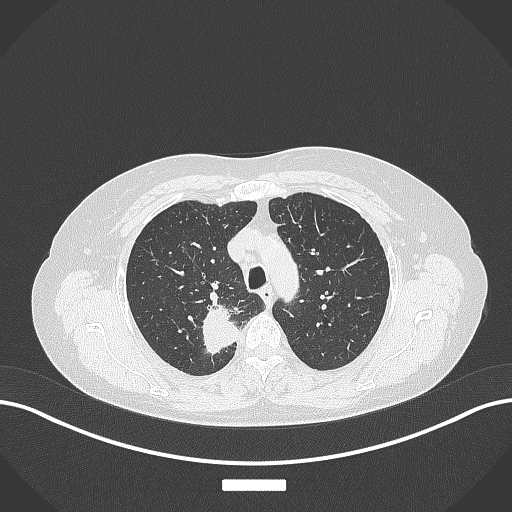
Chest CT, one axial slice. Slice 294 of 357 in the series (ordered by position). Reconstruction kernel B70f. Lung window (W 1500 / L -600 HU). 512 × 512 image matrix. Female patient, age 62 years. From the clinical record (not read from this slice): clinical TNM (as recorded): T1c N1 M0.
Annotated regions visible in this slice (rectangle marked by the reading radiologist):
- lung tumour (recorded histology: squamous cell carcinoma): bounding box [x1, y1, x2, y2] px = [197, 292, 240, 364]